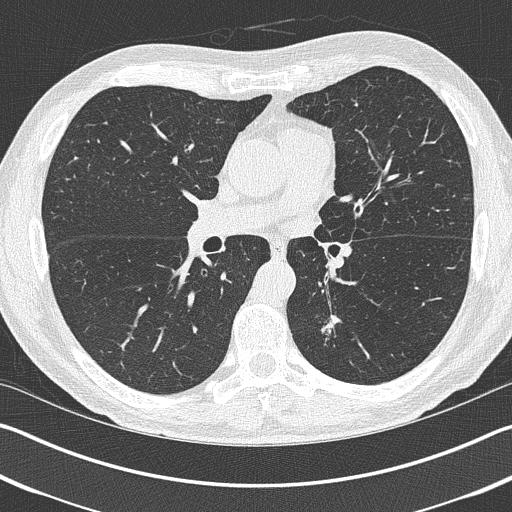
Low-dose screening chest CT, one axial slice; slice 226 of 402 in the series (ordered by position); 120 kVp; lung window (W 1500 / L -600 HU); 512 × 512 image matrix, field of view 340 × 340 mm.
Outlined on this slice (manually delineated by an expert):
- lesion 1 (tumor, lower lobe of left lung): bounding box <322,314,341,340> (left, top, right, bottom; pixels)